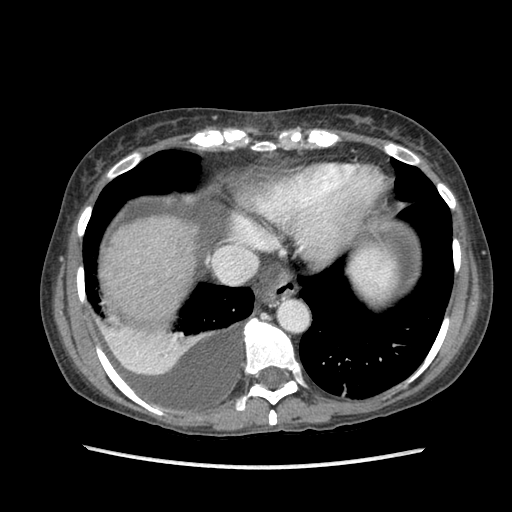
Contrast-enhanced abdominal CT (liver protocol), one axial slice; slice 79 of 87 in the series (ordered by position); reconstruction kernel STANDARD; 120 kVp; soft-tissue window (W 400 / L 40 HU); 2.5 mm slice thickness; 512 × 512 image matrix, field of view 340 × 340 mm. Case-level facts recorded for this patient, not image findings: diagnosis: hepatocellular carcinoma (patient treated with transarterial chemoembolisation; whether this scan precedes or follows treatment is not stated here); TNM stage (as recorded): Stage-IIIB; Child-Pugh class: A; tumour differentiation: no biopsy.
Annotated regions visible in this slice (semi-automatic segmentation, software-assisted and operator-edited):
- liver parenchyma outside the tumour (the mass and vessels are separate outlines, so this box may not span the whole liver): bounding box <100,214,198,300> (left, top, right, bottom; pixels)